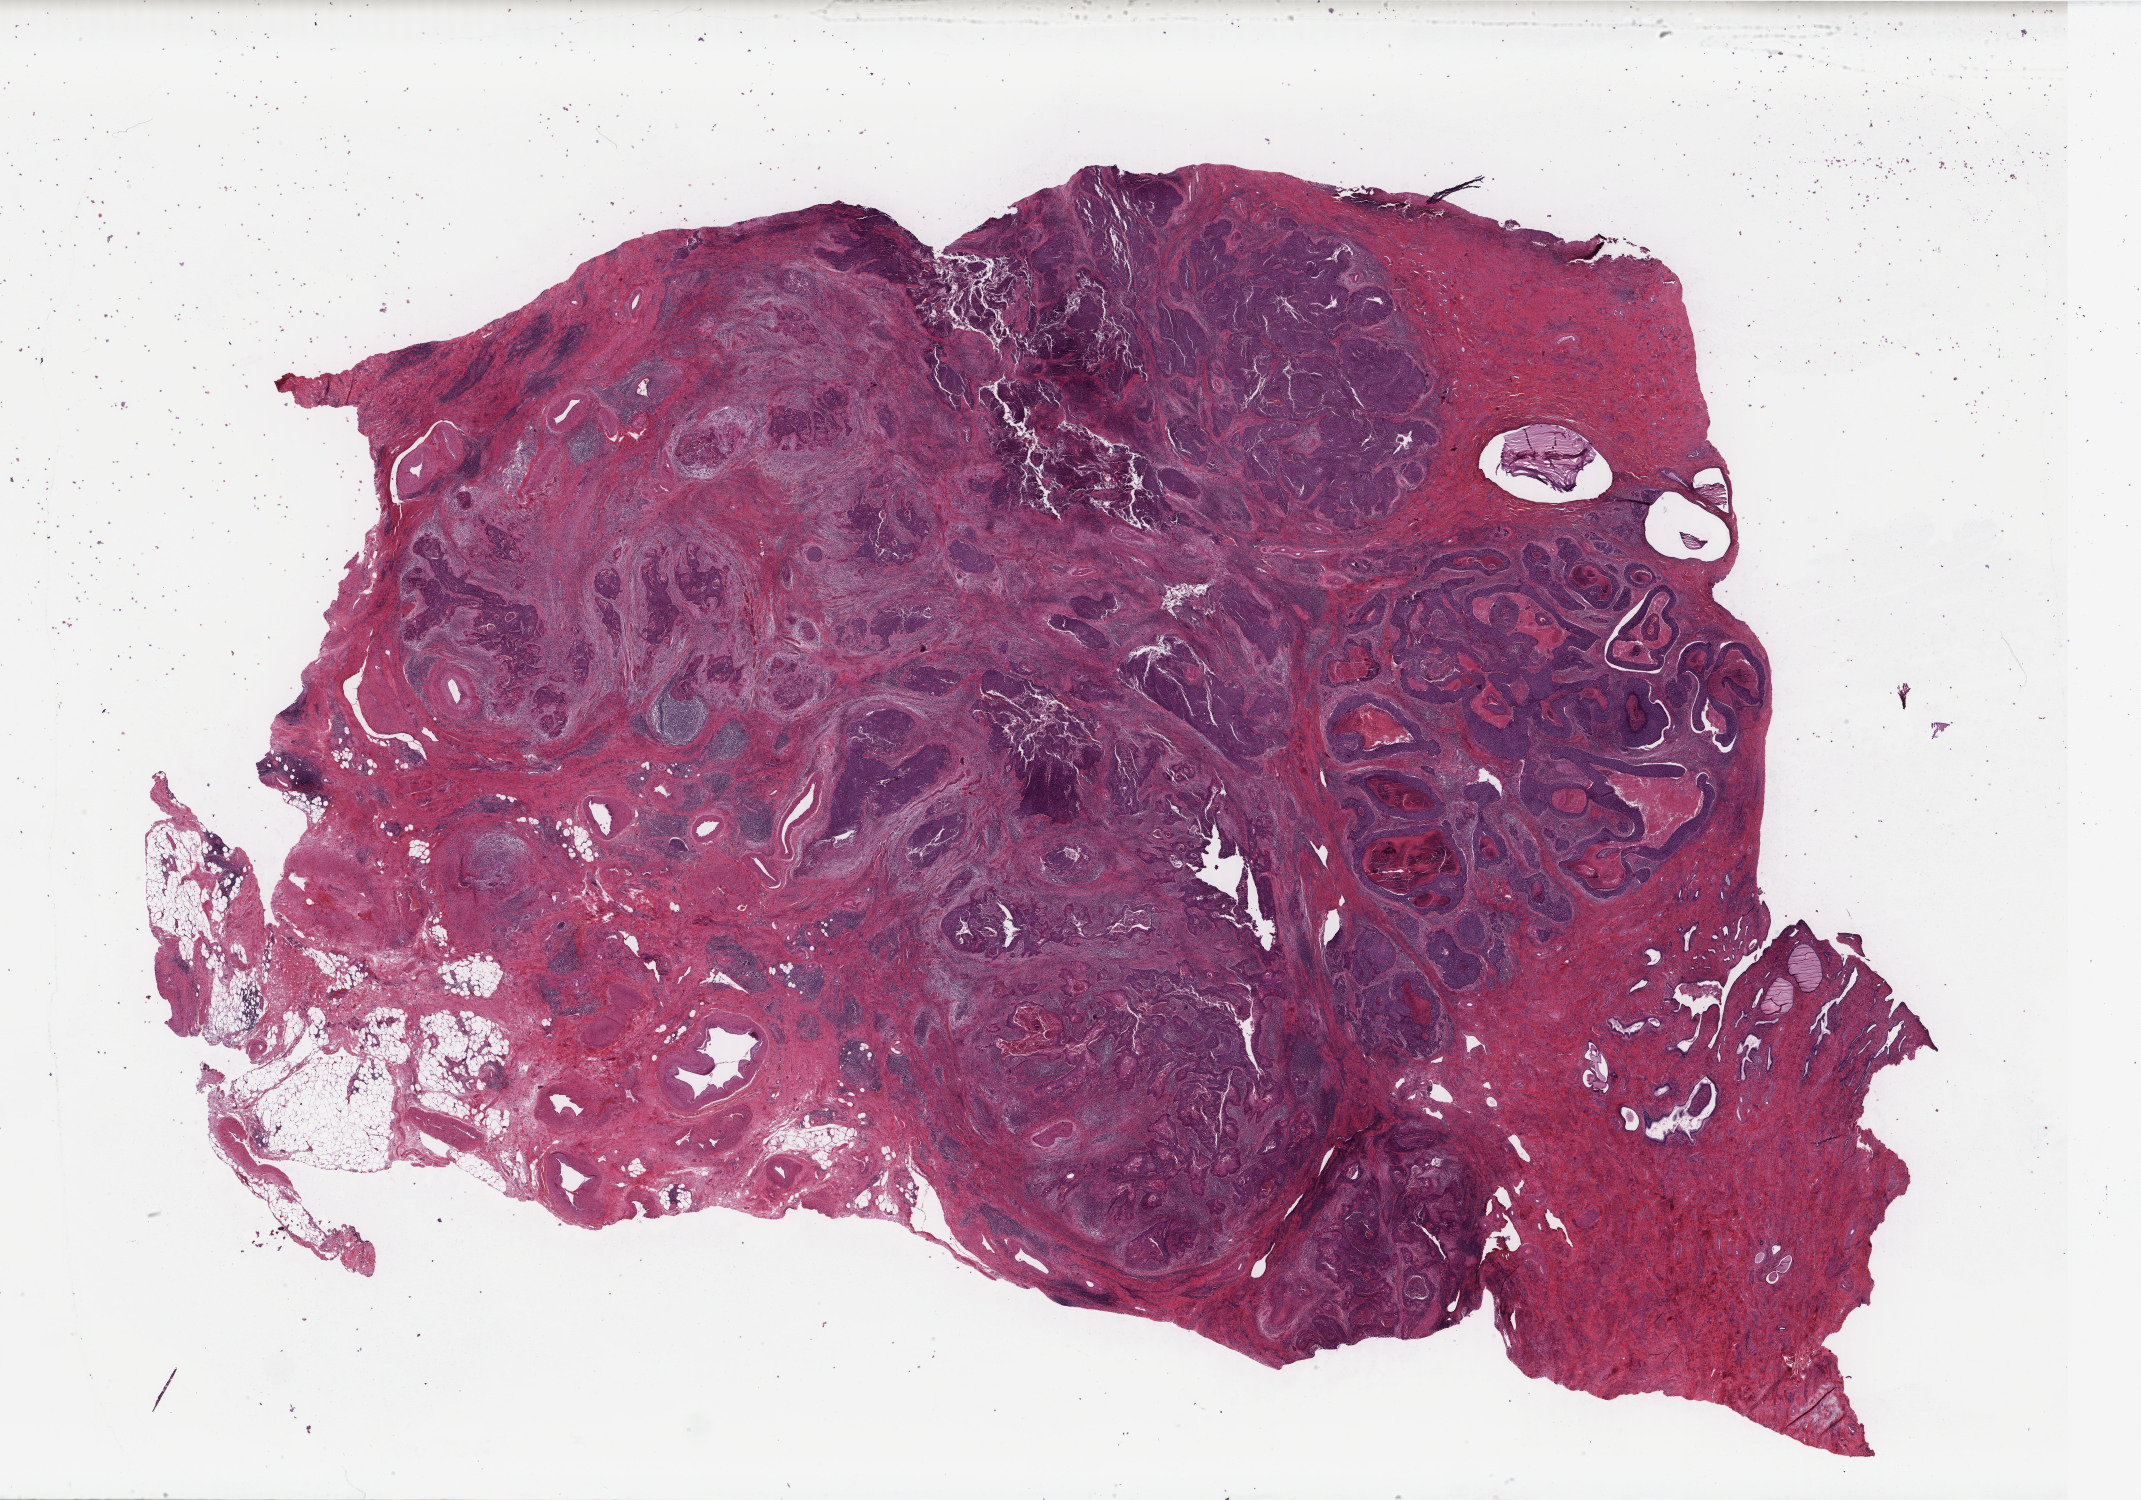
Whole-slide histology image, Hematoxylin and eosin (H&E) stained, low-resolution overview of the scanned area, about 34.0 x 23.8 mm (slide scanned at 40x), formalin-fixed paraffin-embedded (FFPE) diagnostic section, sample: primary tumour, cervix. Female patient; age at initial diagnosis 53 years. Histologic grade: G3 (poorly differentiated).
Diagnosis: Squamous cell carcinoma, NOS (cervix uteri).